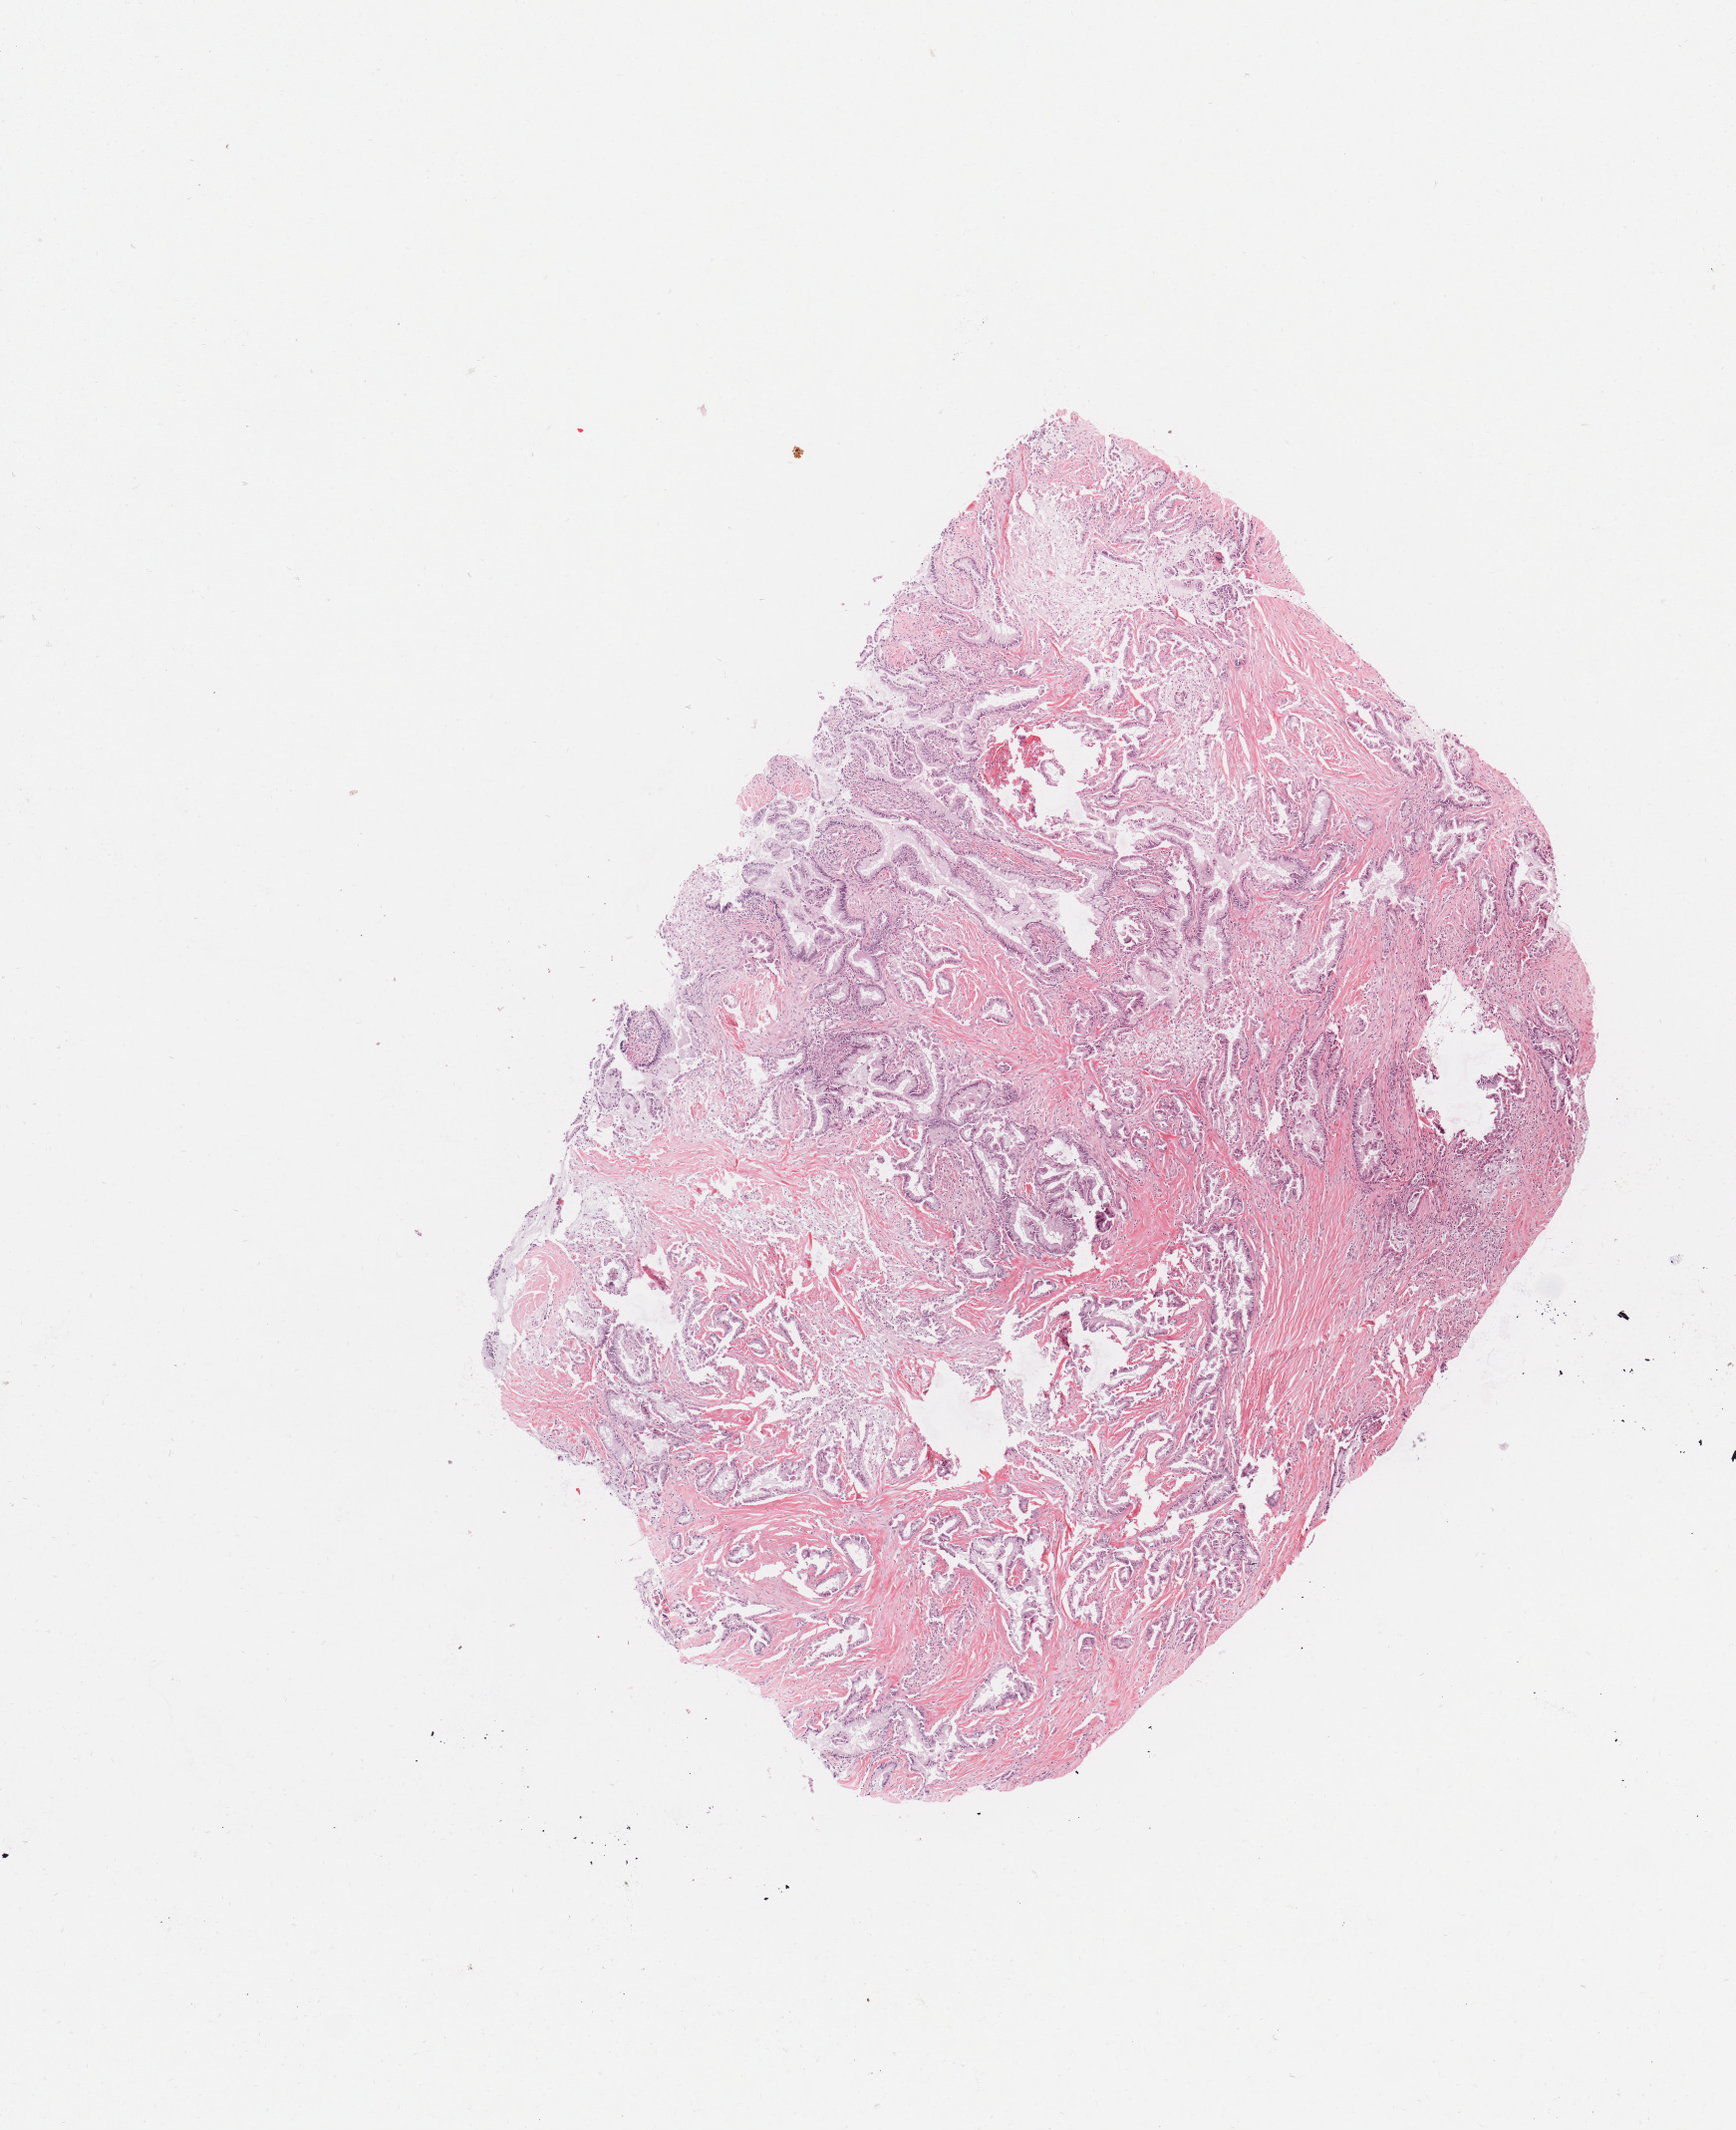
Whole-slide histology image, H&E — whole scanned area (about 6.9 x 8.5 mm, slide scanned at 20x) shown as a low-resolution overview, tumour tissue sample, sampled site: pancreas. 54-year-old female patient. Histologic grade: G2 (moderately differentiated). Pathologist review of this section (percent, as recorded): tumour nuclei 50%, necrosis 0%.
AJCC pathologic stage: IIB. Diagnosis: Infiltrating duct carcinoma, NOS. Primary tumour site (as recorded): head.